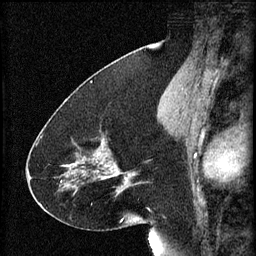
Breast MRI (dynamic contrast-enhanced), one sagittal slice. Position 29 of 60 along the scan axis. 3 images stored at this slice position (order not interpretable as contrast timing). 1.5 T. TE 4.2 ms, TR 8.2 ms. 256 × 256 image matrix, field of view 180 × 180 mm. Patient: female, 41 years.
Structures marked on this image (semi-automatically segmented with operator editing):
- analysis volume of interest (the breast-tissue region the enhancement analysis was run in; not a lesion): bounding box <72,122,134,195> (left, top, right, bottom; pixels)
- tumour enhancement mask (voxels above the 70 % enhancement threshold inside the analysis volume of interest): <75,140,134,191>